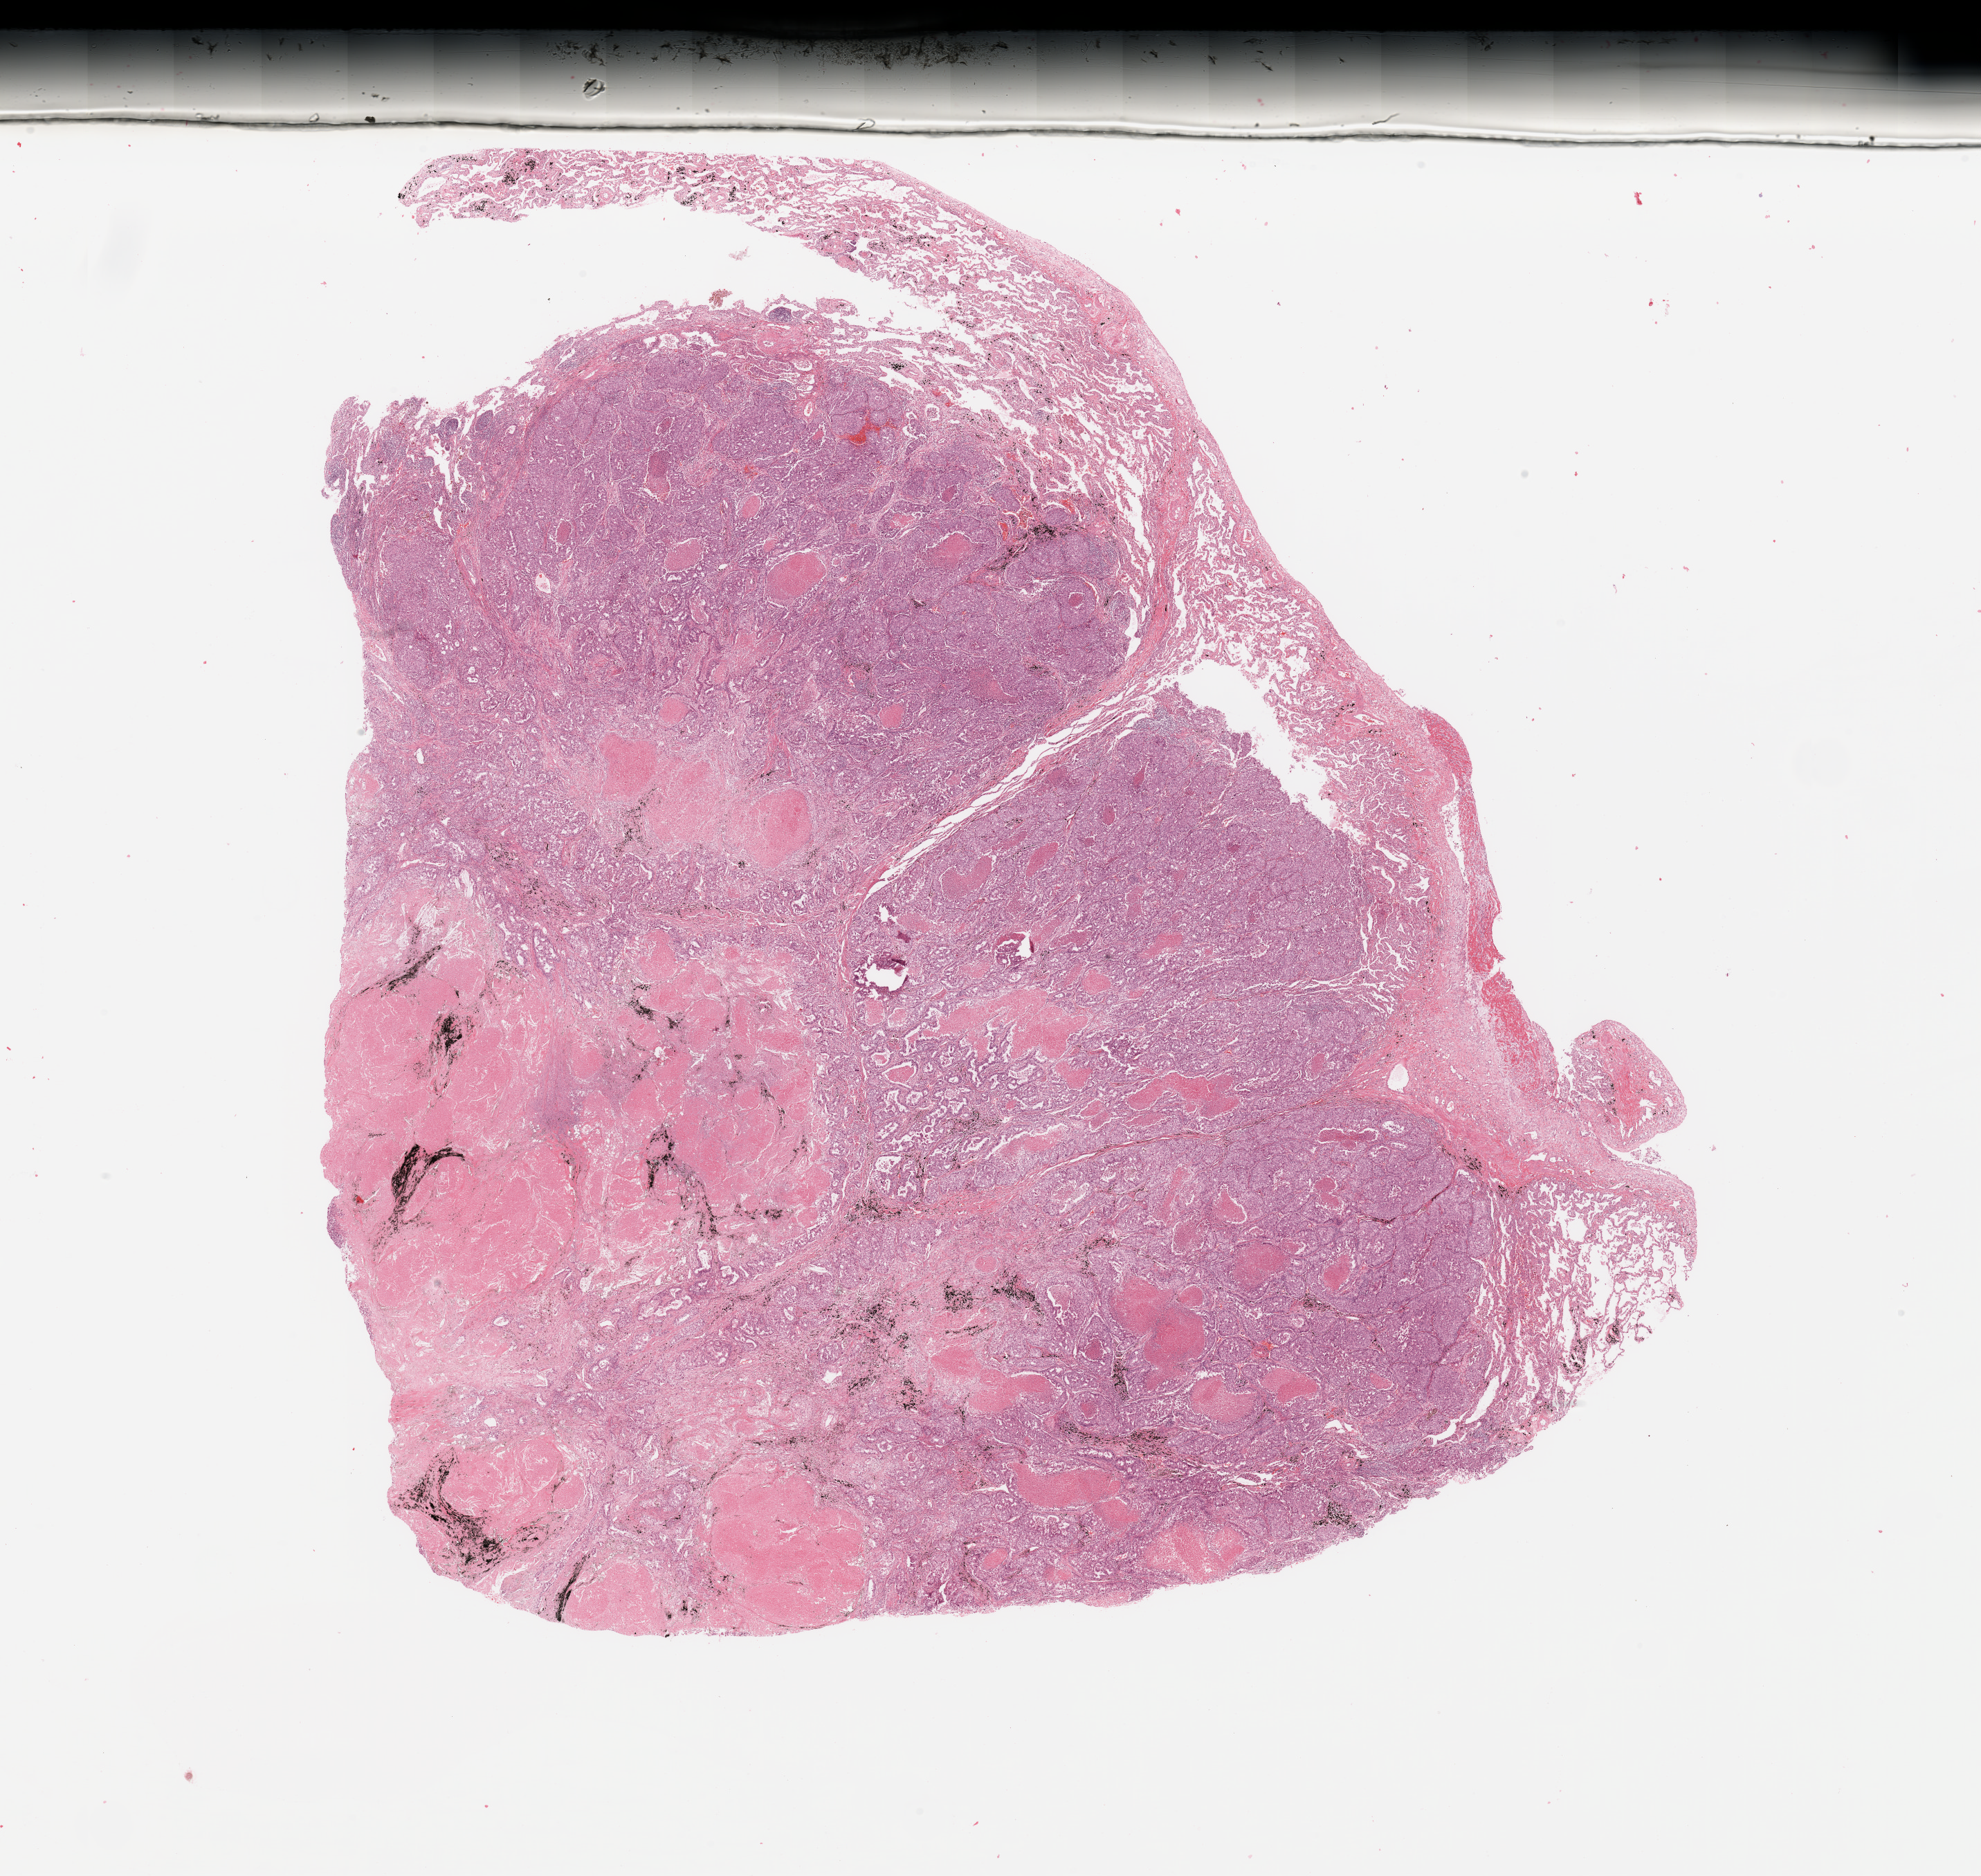
H&E whole-slide image, a low-resolution overview of the entire scanned area, about 22.6 x 21.4 mm (from a 20x scan); lung, tumour tissue. 55-year-old male patient. Histologic grade: G3 (poorly differentiated).
• AJCC pathologic stage: IIIA
• diagnosis: Adenocarcinoma, NOS